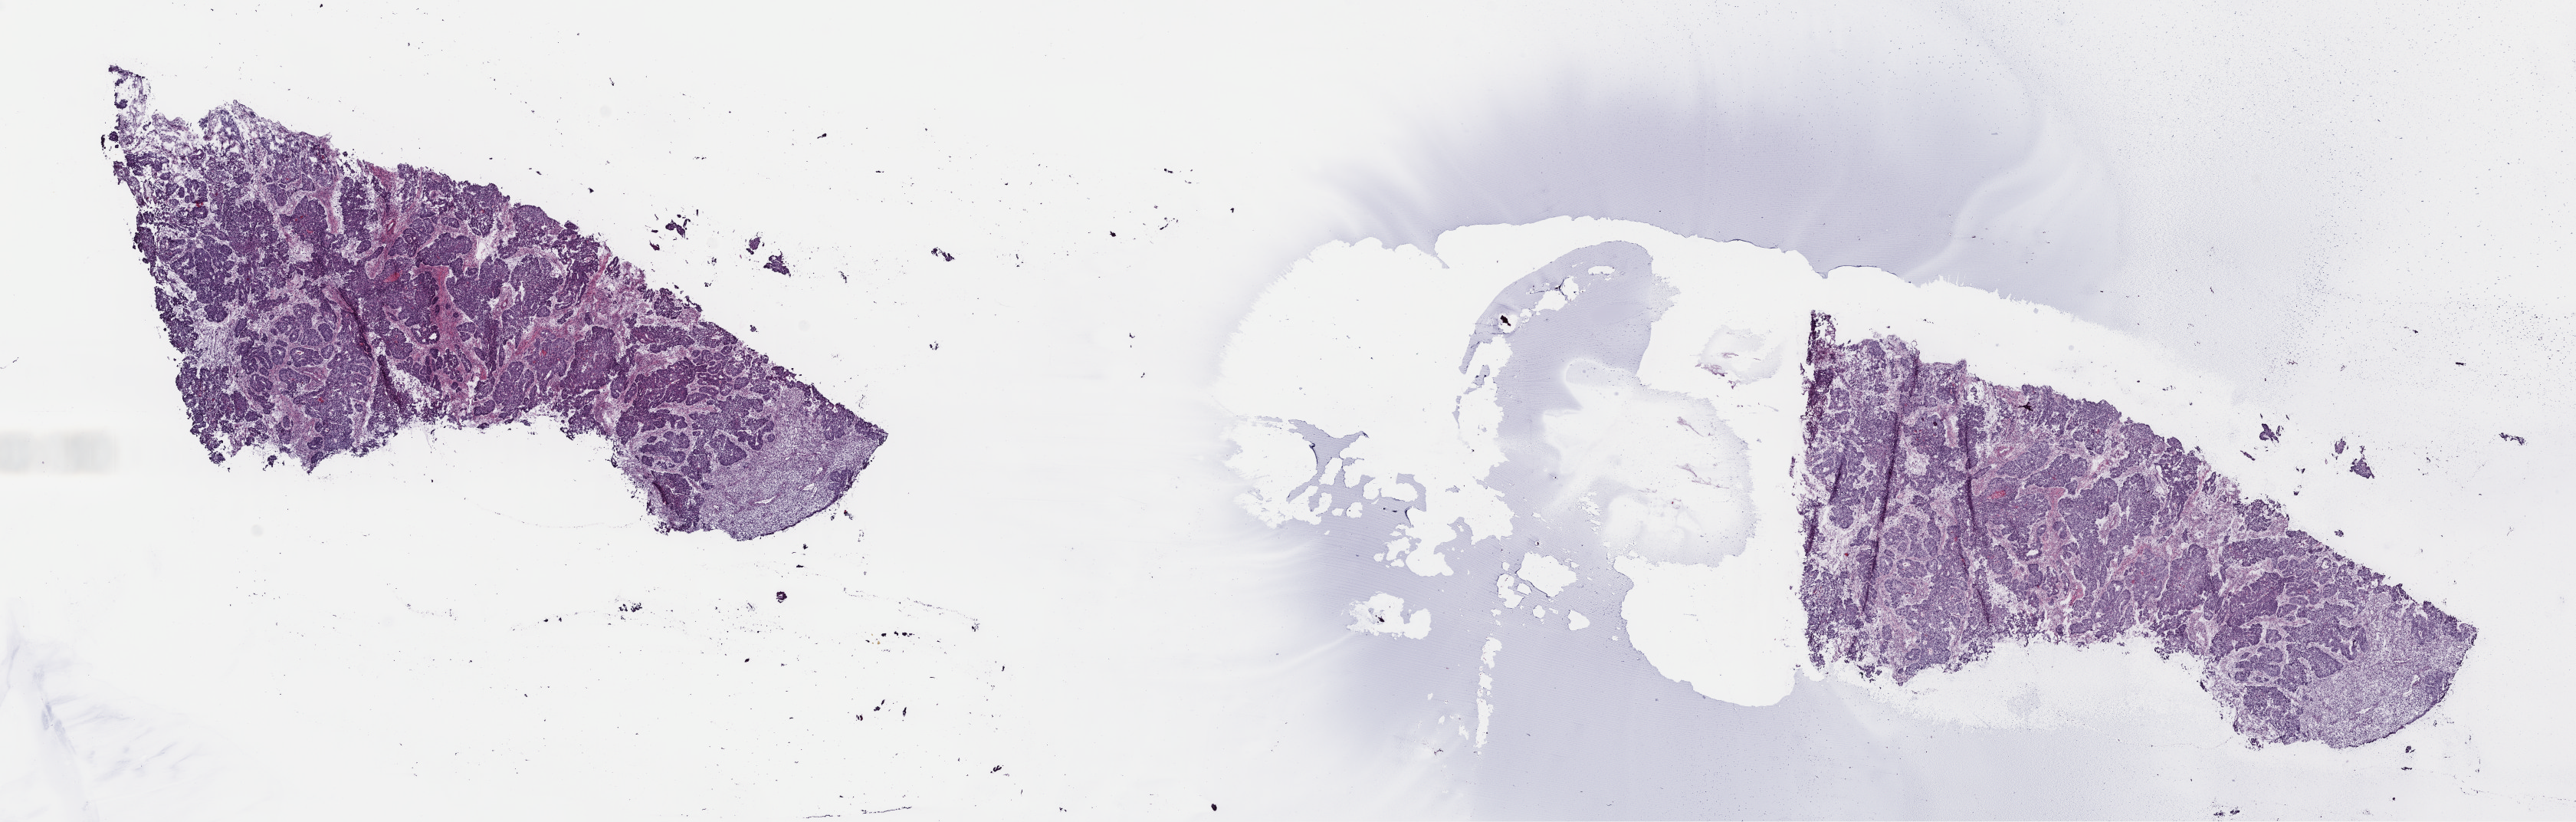
Whole-slide histology image, H&E, a low-resolution overview of the entire scanned area, about 26.4 x 8.4 mm. Frozen section from the top of the tissue portion. Sample: primary tumour, uterus. Female, age 42 years at initial diagnosis. Histologic grade: G3 (poorly differentiated). Composition of this section per pathologist review: tumour cells 100%, tumour nuclei 75%, normal cells 0%, stromal cells 0%, necrosis 0%. Inflammatory infiltration, as recorded: lymphocyte infiltration 3%, monocyte infiltration 0%, neutrophil infiltration 0%.
FIGO stage: IA. Pathologic diagnosis: Endometrioid adenocarcinoma, NOS (endometrium).